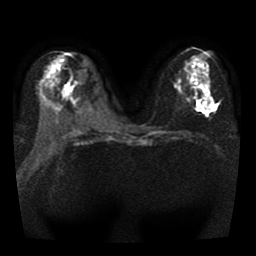
Breast MRI, one axial slice. Diffusion-weighted series; image 2 of 4 stored at this slice position (different b-values; order by instance number). 1.5 T. 5 mm slice thickness. 256 × 256 image matrix, field of view 330 × 330 mm. Female patient.
Annotated regions visible in this slice (manually delineated by an expert):
- tumour on diffusion-weighted imaging: box from (x=203, y=94) to (x=213, y=110) px